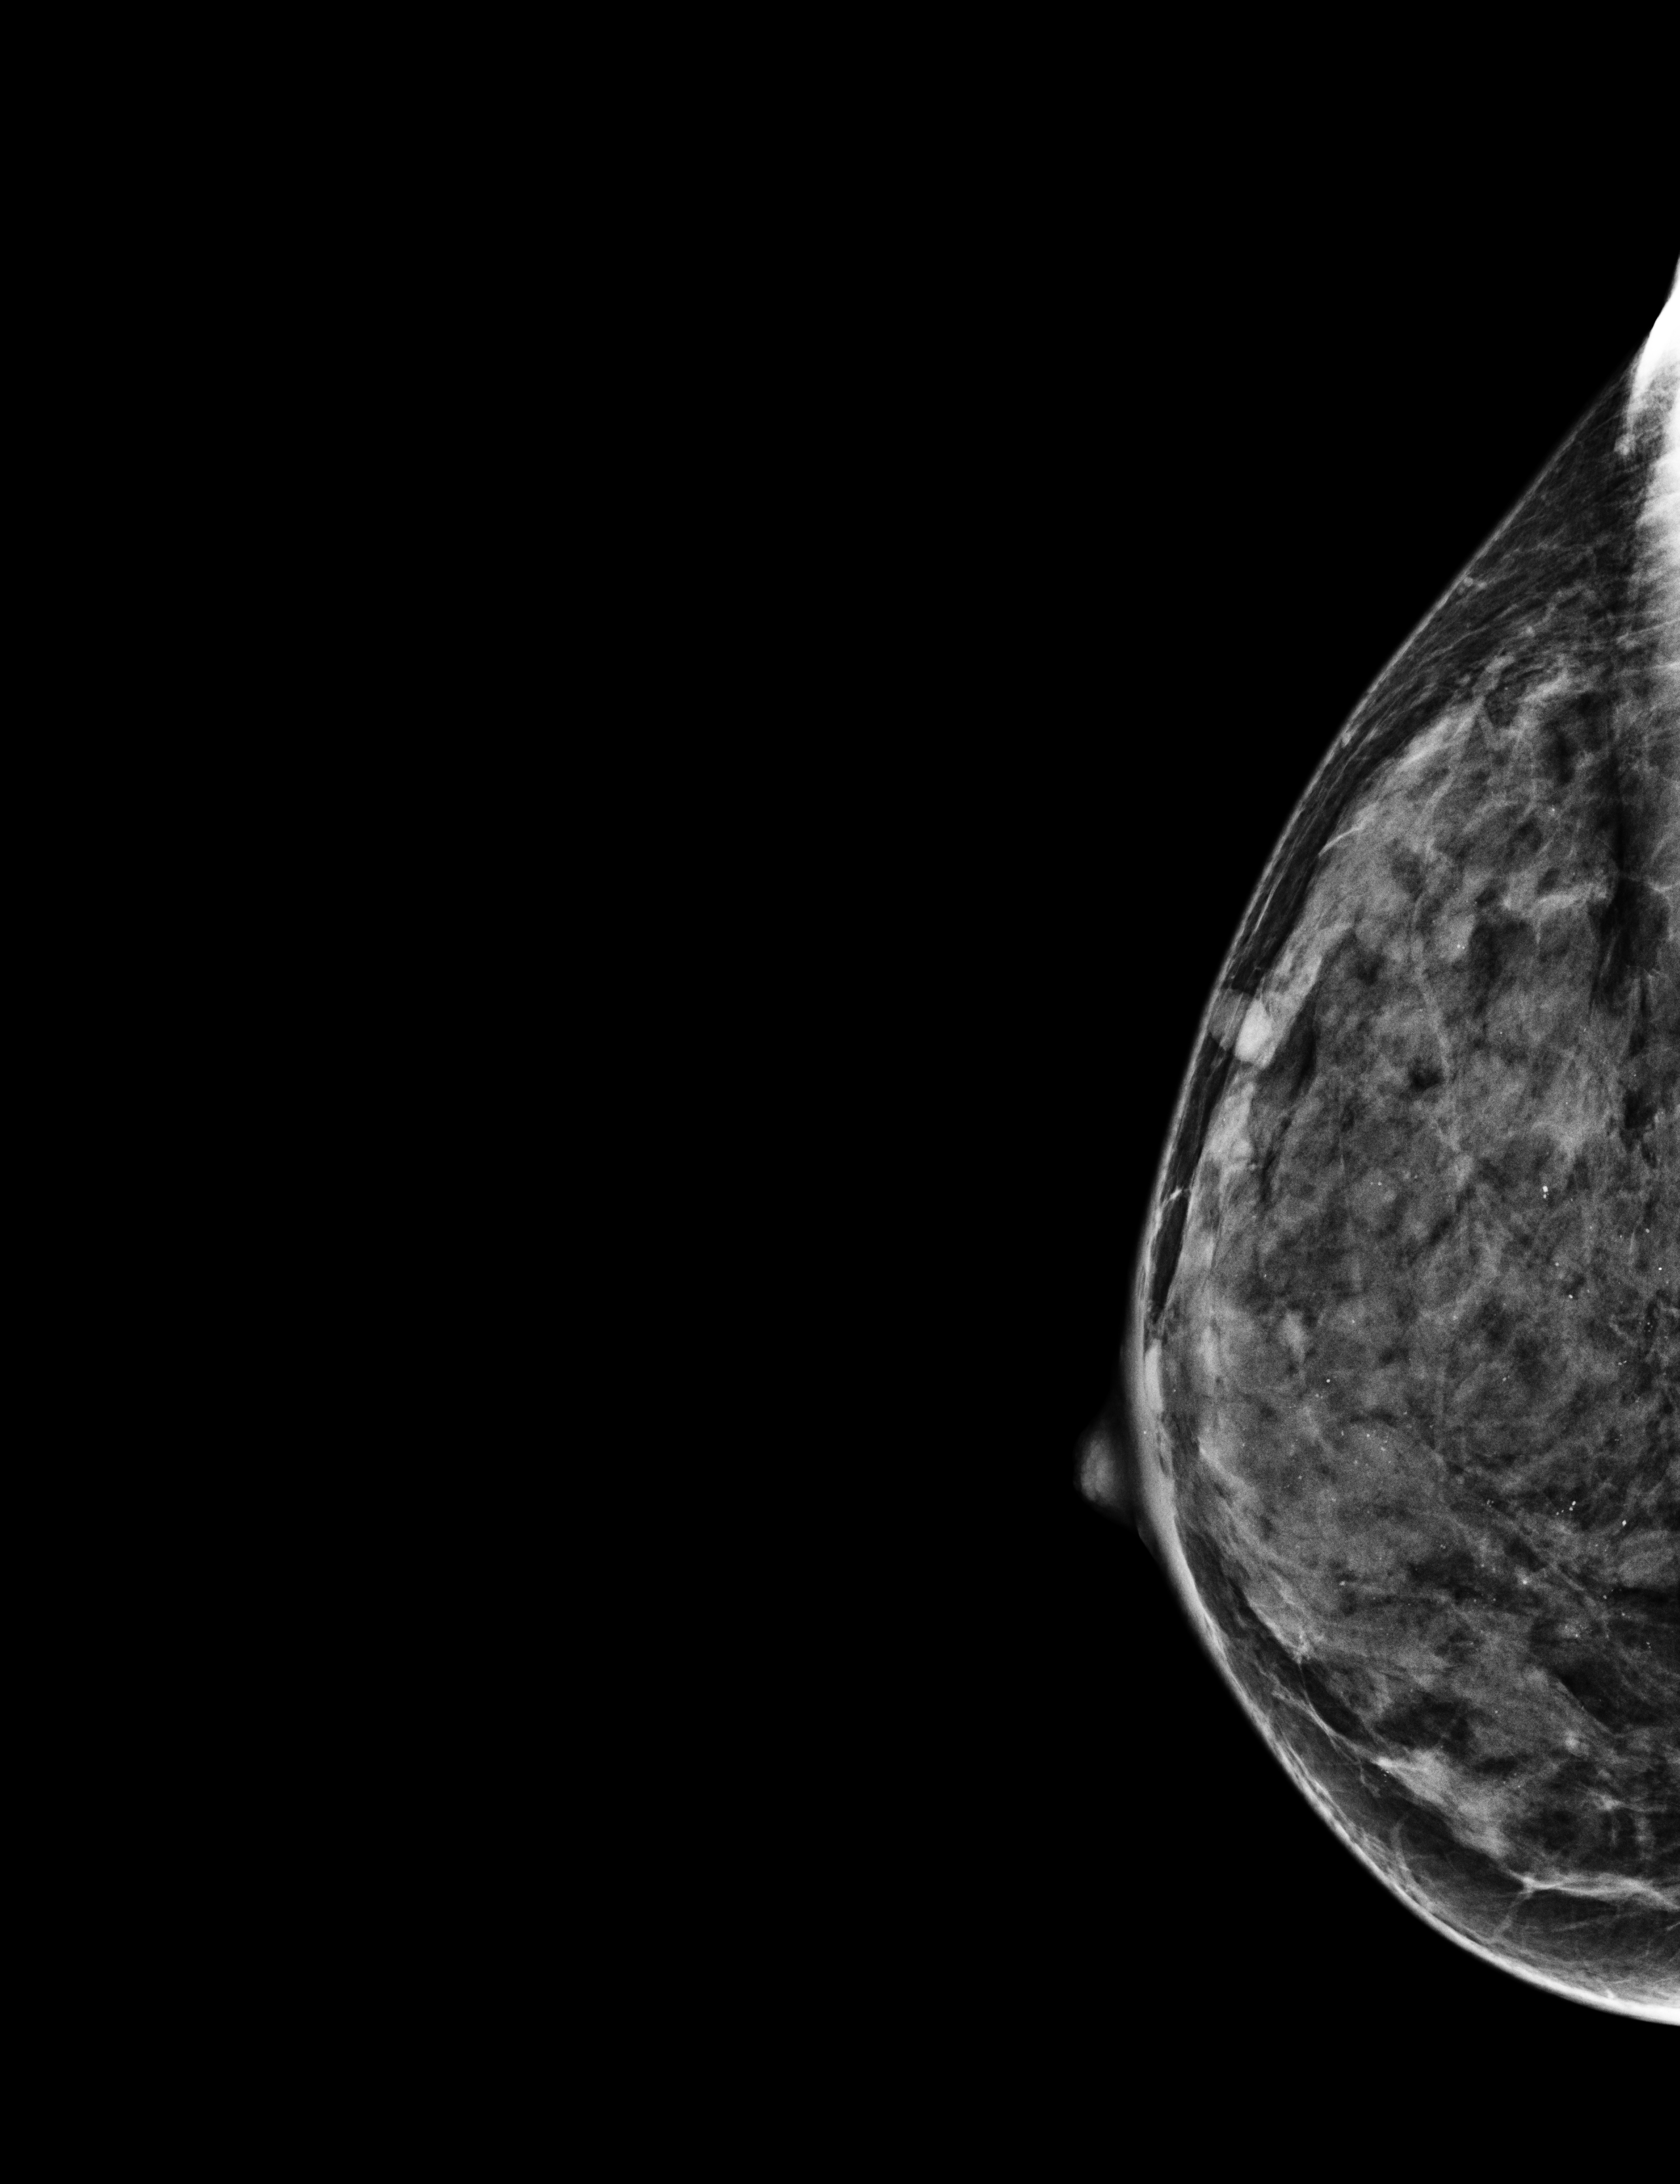
Full-field digital mammogram (FFDM); right breast; exaggerated CC view (lateral); screening examination. Patient: female, 49 years.
- BI-RADS breast density category at the screening exam (both breasts, scale 1–4): 4
- final BI-RADS category for the screening round (tomosynthesis exam, both breasts): category 2
- recall: no recall after this screen